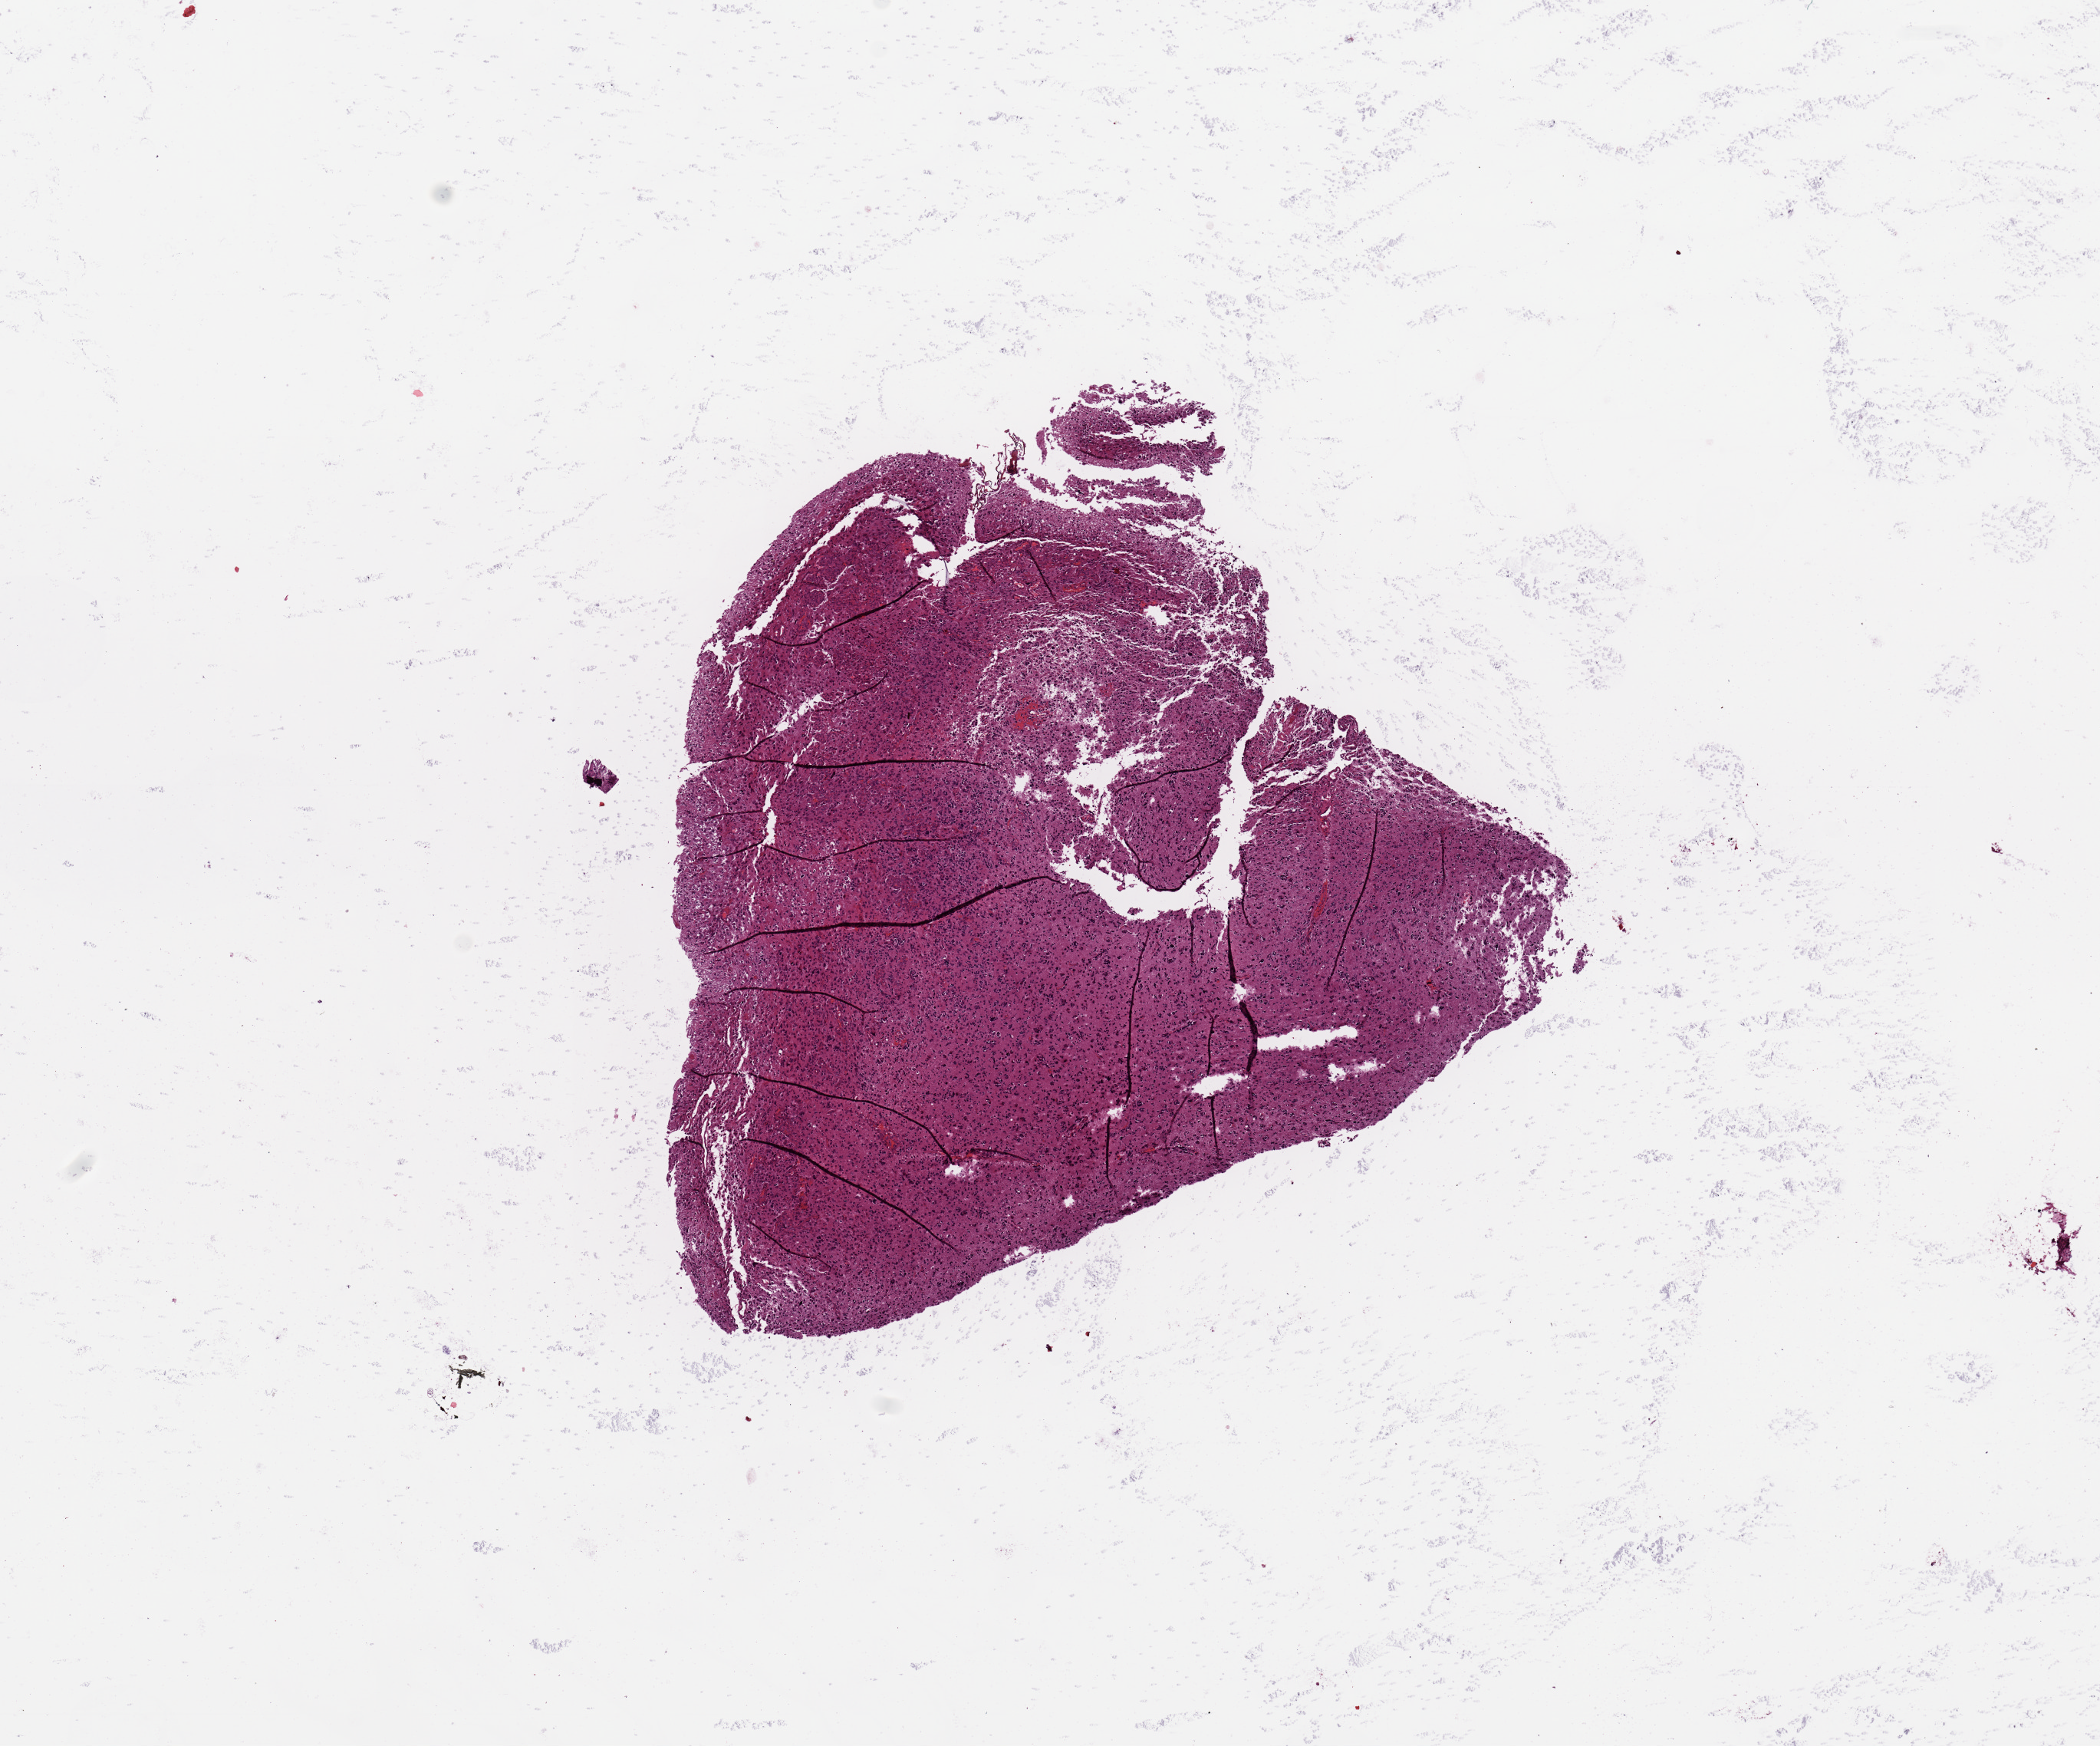
Digitized H&E-stained tissue section (whole slide) — a low-resolution overview of the entire scanned area, about 10.8 x 9.0 mm (from a 20x scan). Tumour tissue sample, sampled site: brain. Male, 64 y/o. Pathologist review of this section (percent, as recorded): tumour nuclei 90%, necrosis 3%.
- diagnosis: Glioblastoma
- primary tumour site (as recorded): temporal lobe